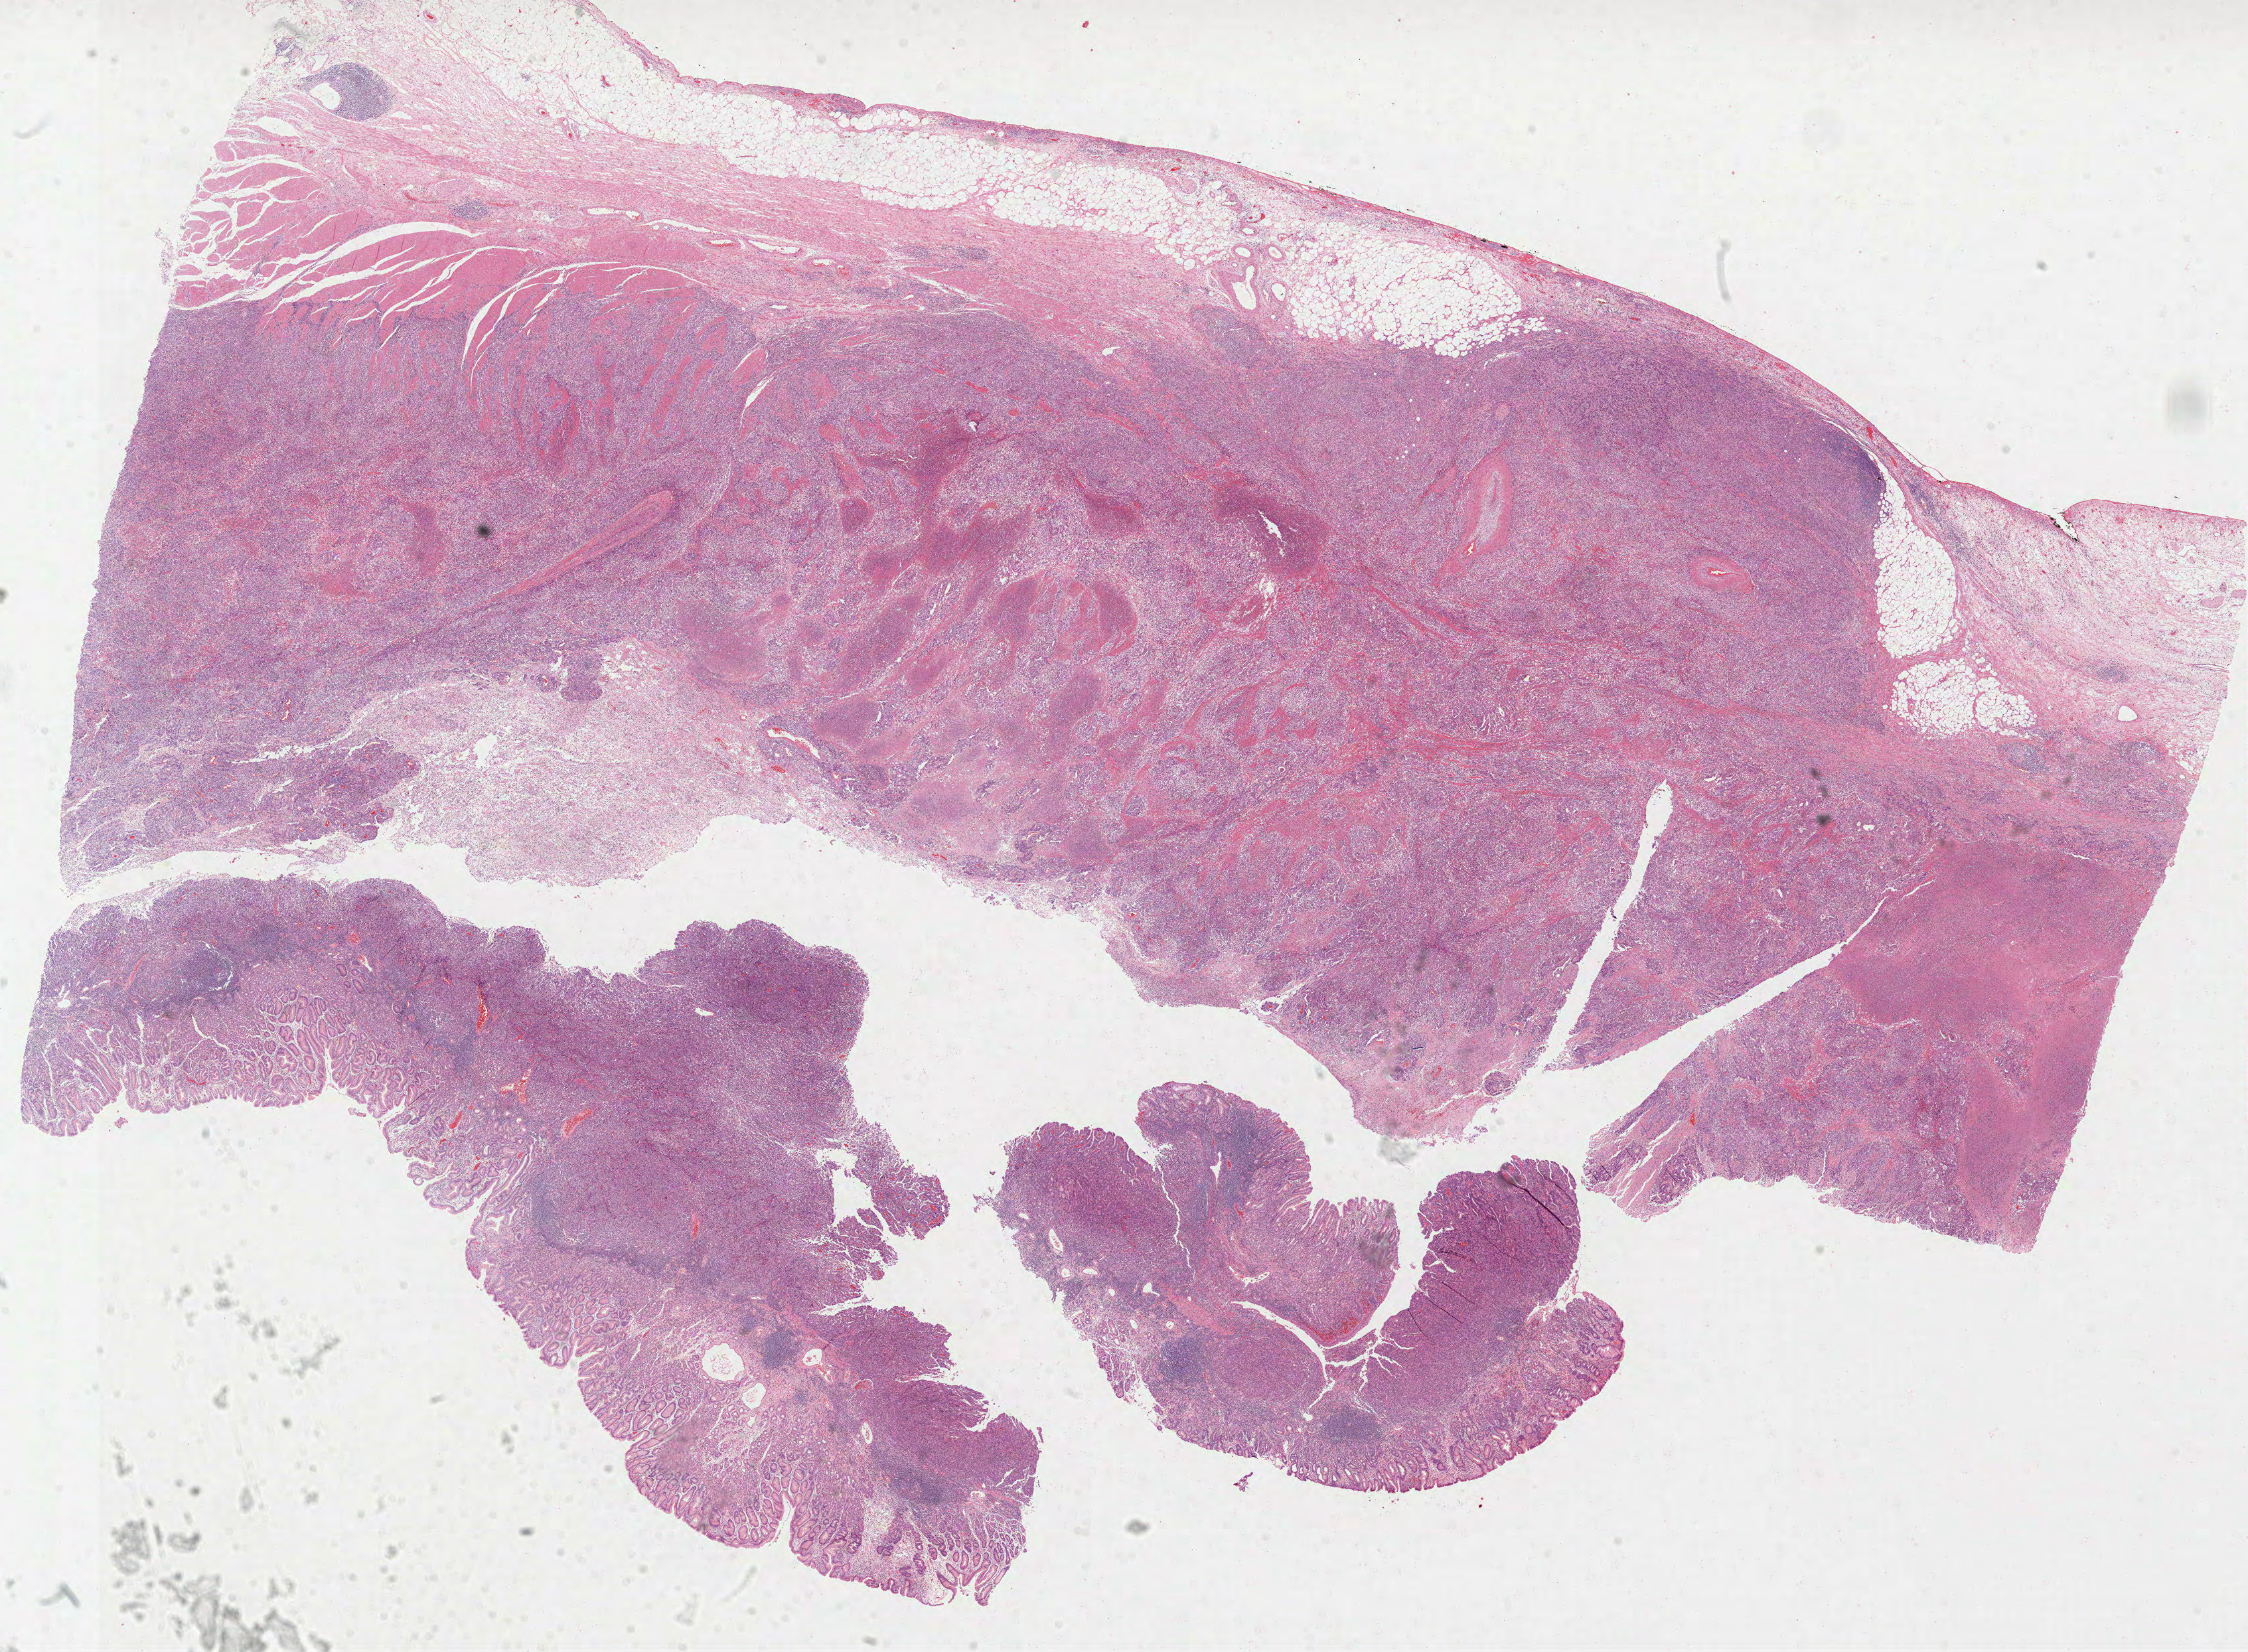
H&E-stained whole-slide image, low-resolution overview of the scanned area, about 27.3 x 20.1 mm (slide scanned at 40x), formalin-fixed paraffin-embedded (FFPE) diagnostic section, sample: primary tumour, stomach. Female patient; age at initial diagnosis 71 years. Histologic grade: G3 (poorly differentiated).
TNM: T2b N0 MX. Lymph nodes positive (case pathology): 0 of 37 examined. AJCC pathologic stage: IB (6th edition). Histologic diagnosis: Signet ring cell carcinoma (body of stomach).